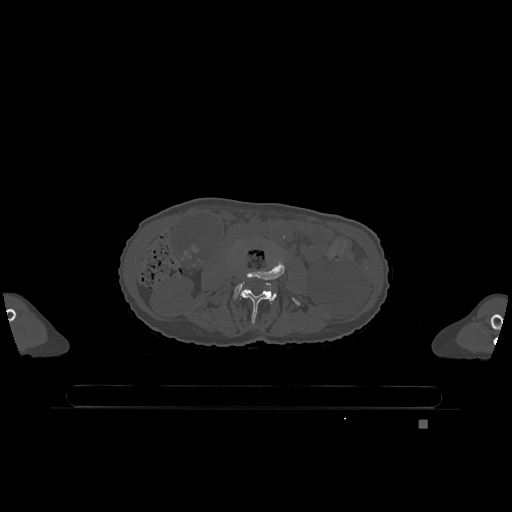
CT including the spine, one axial slice; slice 343 of 1317 in the series (ordered by position); bone window (W 1800 / L 400 HU); 0.5 mm slice thickness; 512 × 512 image matrix, field of view 500 × 500 mm. Patient: female, 74 years. Case-level facts recorded for this patient, not image findings: primary cancer: lung.
Outlined on this slice (semi-automatic segmentation, software-assisted and operator-edited):
- L3 vertebra: bounding box <240,258,301,323> (left, top, right, bottom; pixels)
- L4 vertebra: <233,282,277,300>